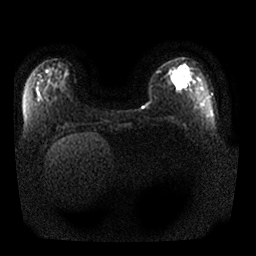
Breast MRI, one axial slice. Position 7 of 25 along the scan axis. Diffusion-weighted series; image 2 of 4 stored at this slice position (different b-values; order by instance number). 1.5 T. 256 × 256 image matrix, field of view 350 × 350 mm. Female patient.
Outlined on this slice (expert manual segmentation):
- tumour on diffusion-weighted imaging: bounding box (x1, y1, x2, y2) in pixels: (172, 69, 180, 81)